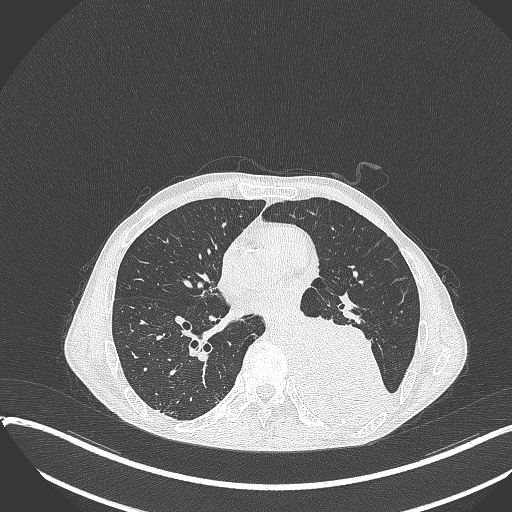
Chest CT, one axial slice. Slice 166 of 401 in the series (ordered by position). Reconstruction kernel B70f. 120 kVp. Lung window (W 1500 / L -600 HU). 1 mm slice thickness. 512 × 512 image matrix, field of view 400 × 400 mm. Male patient, age 57 years. From the clinical record (not read from this slice): clinical TNM (as recorded): T4 N0 M0.
Outlined on this slice (rectangle marked by the reading radiologist):
- lung tumour (recorded histology: squamous cell carcinoma): box from (x=292, y=311) to (x=398, y=428) px